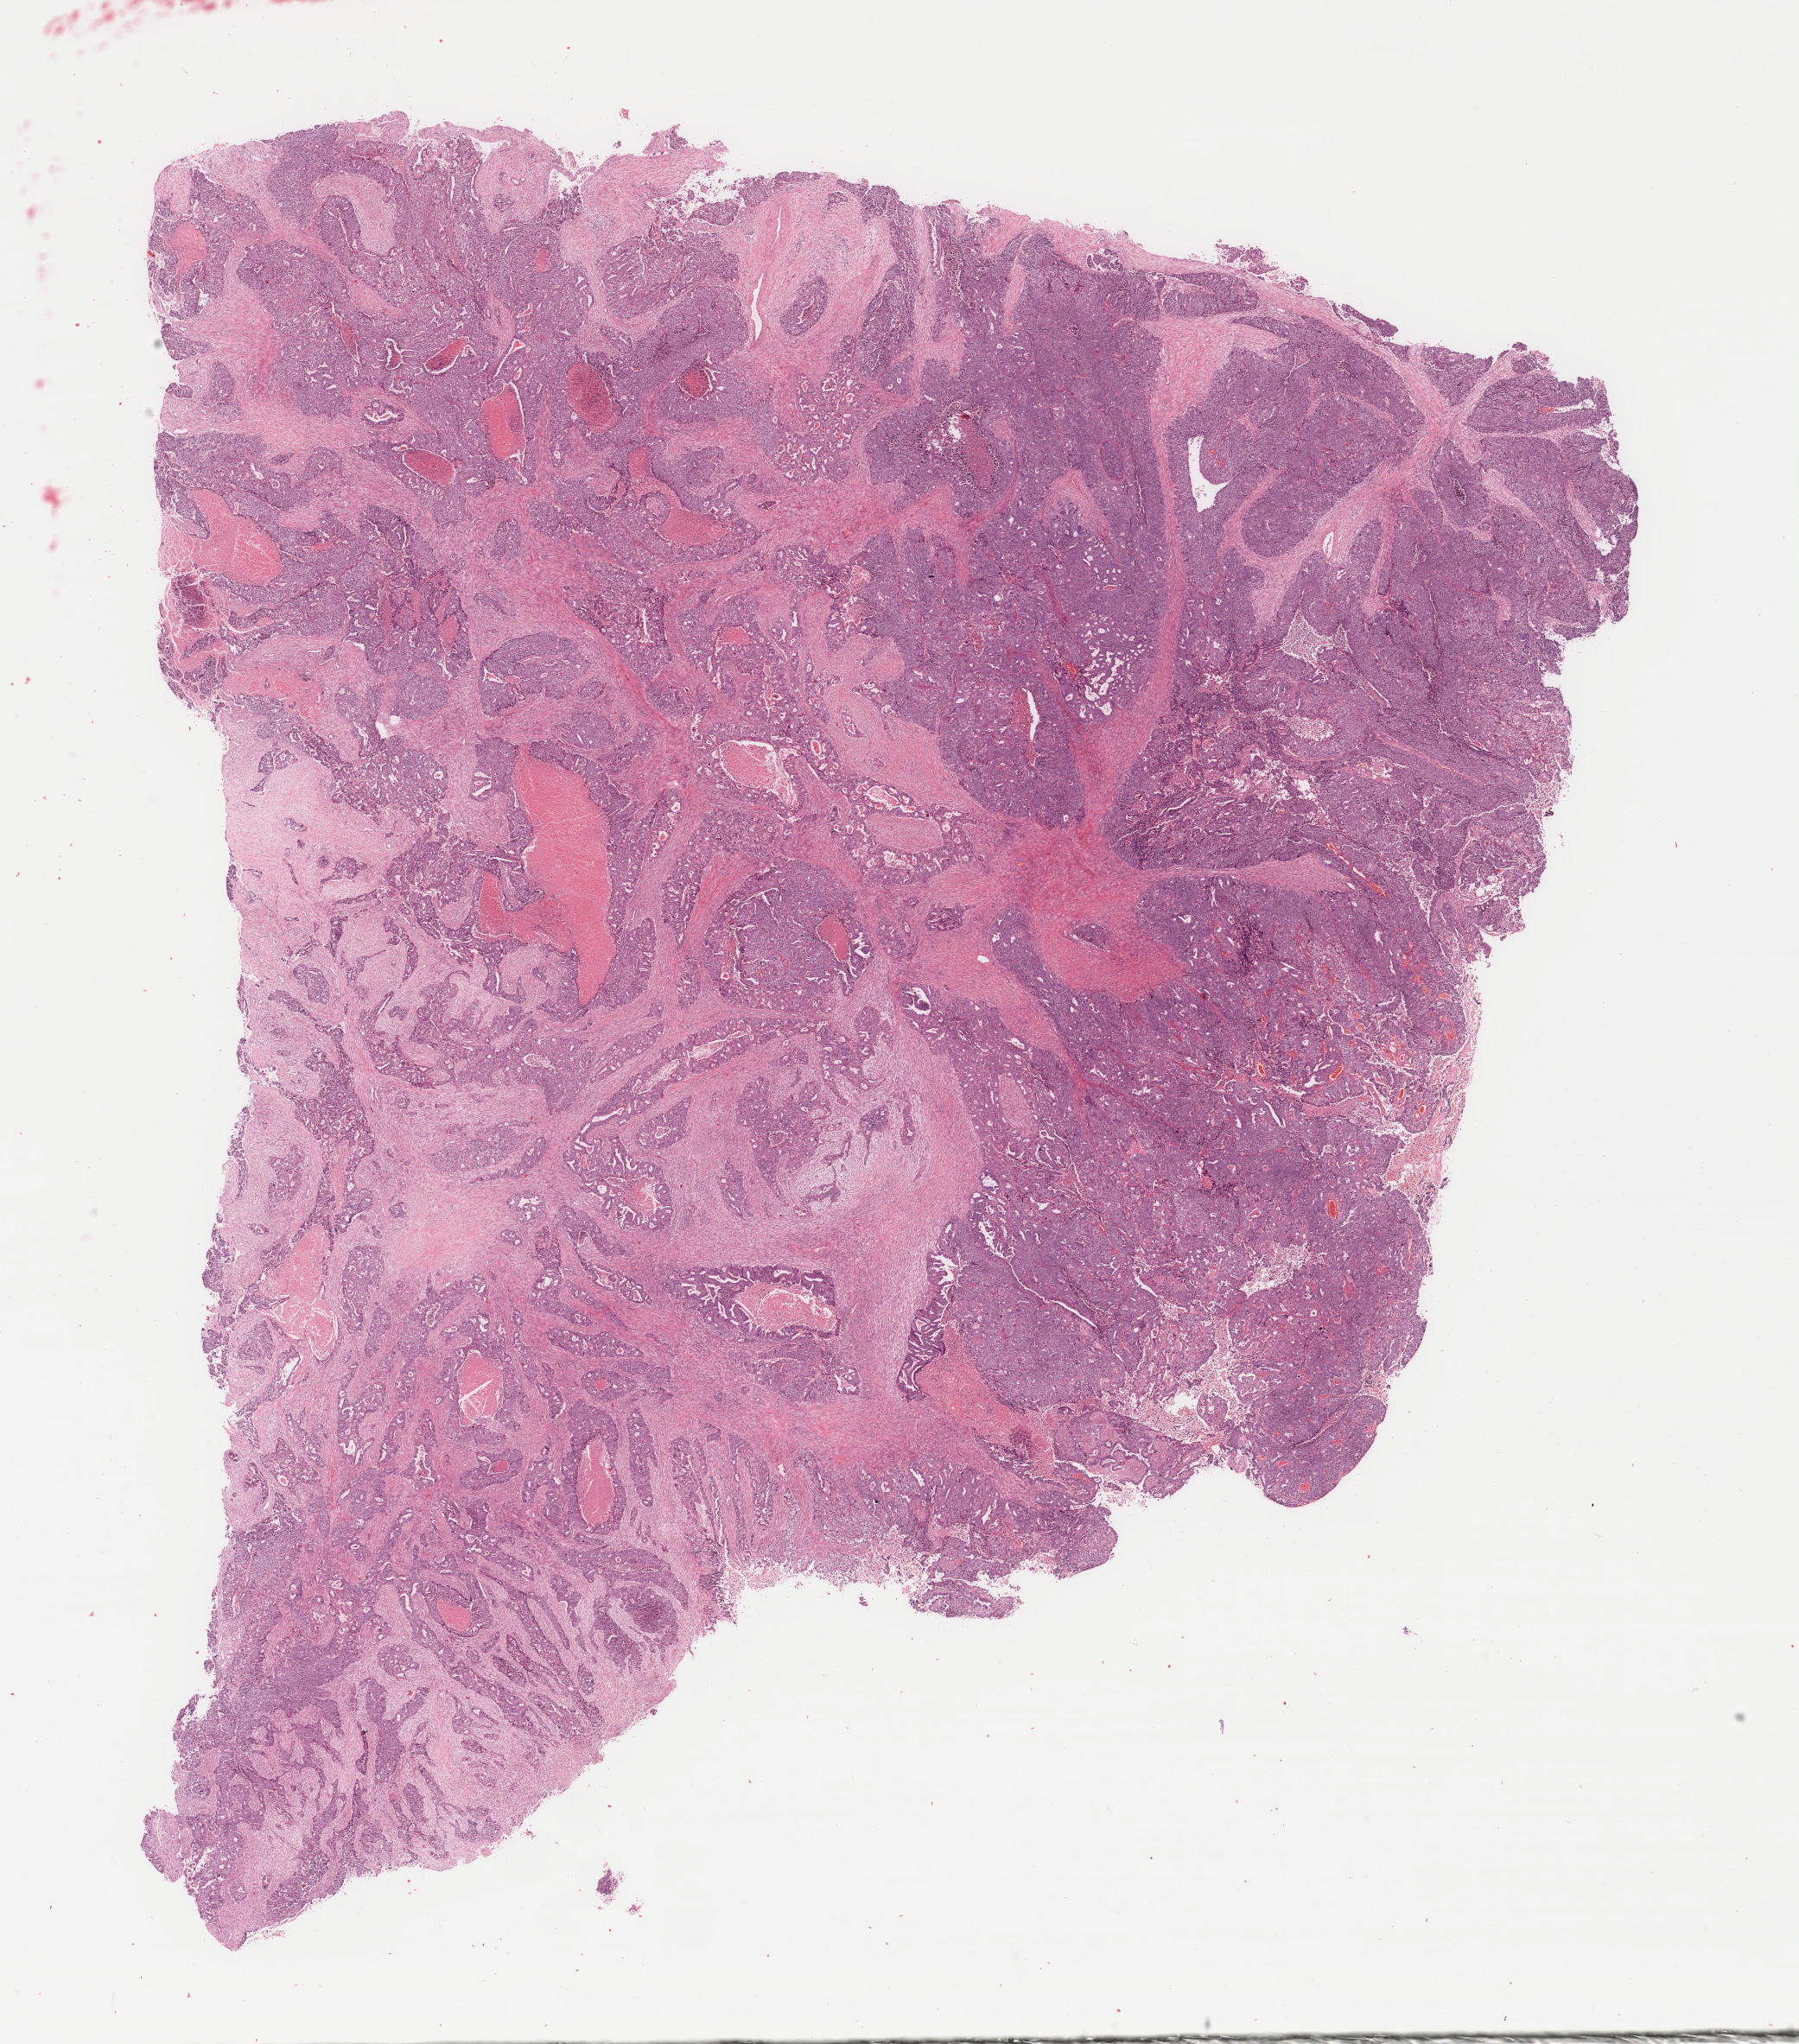
Digitized H&E-stained tissue section (whole slide), shown as a low-resolution overview of the whole scanned area (about 16.5 x 18.8 mm, acquisition: 40x scan). Formalin-fixed paraffin-embedded (FFPE) diagnostic section. Primary tumour sample from the cervix. Female patient; age at initial diagnosis 38 years. Histologic grade: G3 (poorly differentiated).
FIGO stage: IB1. Lymph nodes positive (case pathology): 0 of 7 examined. Pathologic diagnosis: Endometrioid adenocarcinoma, NOS (cervix uteri).